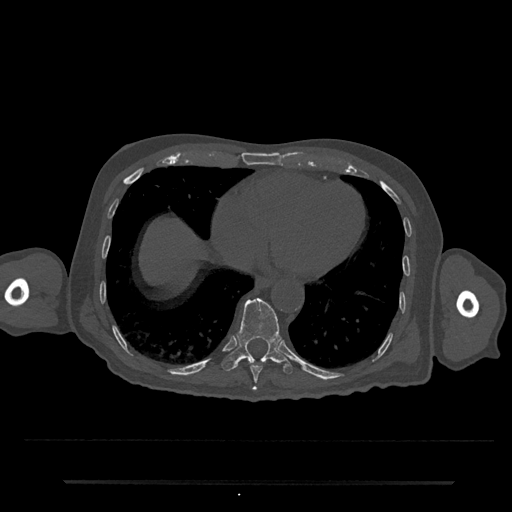
CT including the spine, one axial slice; position 330 of 797 along the scan axis; reconstruction kernel Br40s/3; 120 kVp; bone window (W 1800 / L 400 HU); 0.5 mm slice thickness; 512 × 512 image matrix. Male patient, age 74 years. Case-level facts recorded for this patient, not image findings: primary cancer: prostate.
Structures marked on this image (semi-automatic segmentation, software-assisted and operator-edited):
- T10 vertebra: bounding box [x1, y1, x2, y2] px = [222, 298, 293, 374]
- T9 vertebra: [250, 361, 263, 391]